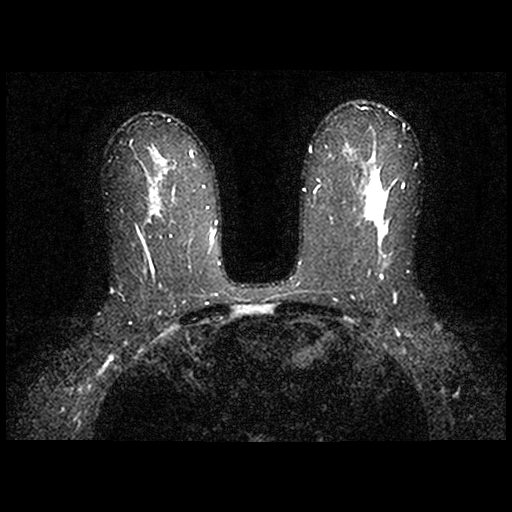
MRI of the breasts; 2 images, each one mid-volume slice chosen by position. Patient in her 40s.
Image 1: axial T2-weighted / STIR image, series "STIR SENSE", slice 43 of 84, 2 mm slice thickness.
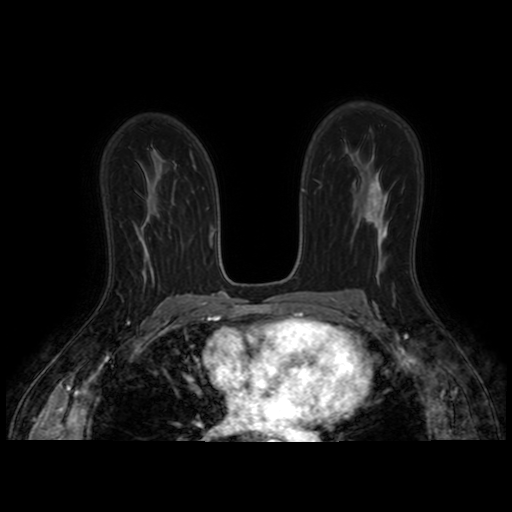
Image 2: axial dynamic contrast-enhanced T1-weighted image, series "AX BLISS_AUTO SENSE", slice 43 of 84, dynamic phase 5 of 8.
Pathology recorded for this patient (not read from these images): pathology diagnosis: invasive intraductal (left breast); clinical background (as recorded): history of left breast cancer (invasive ductal cancer), status post left partial mastectomy.